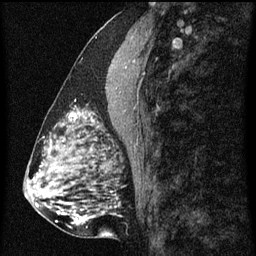
Breast MRI (dynamic contrast-enhanced), one sagittal slice. Position 24 of 60 along the scan axis. Dynamic contrast-enhanced series, image 2 of 3 at this slice position (ordered by acquisition). 1.5 T. TE 4.2 ms, TR 8 ms. 2 mm slice thickness. 256 × 256 image matrix. Patient: female, 51 years.
Structures marked on this image (semi-automatic segmentation, software-assisted and operator-edited):
- analysis volume of interest (the breast-tissue region the enhancement analysis was run in; not a lesion): bounding box <61,110,102,129> (left, top, right, bottom; pixels)
- tumour enhancement mask (voxels above the 70 % enhancement threshold inside the analysis volume of interest): <69,112,93,123>